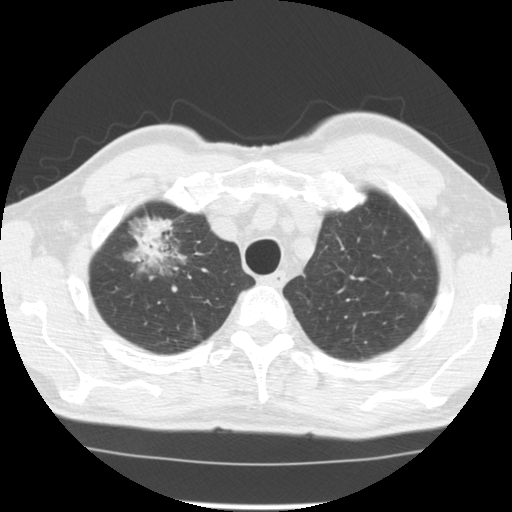
Axial slice from a low-dose chest CT screening exam; third annual screen; lung window (W 1500 / L -600 HU); 2.5 mm slice thickness; standard (soft-tissue) reconstruction kernel (STANDARD); 120 kVp; slice 24 of 128 in the series; 512 × 512 image matrix. Male participant, aged 64 years at enrolment. Former smoker at enrolment.
Lesion marked by an expert reader, box from (x=124, y=227) to (x=198, y=288) px. The screening reader recorded 3 non-calcified nodules or masses ≥4 mm on this exam; which of them this box marks is not recorded. Official screen result: positive, other. Later outcome: lung cancer diagnosed 30 days after this screen — adenocarcinoma, NOS, right upper lobe, well differentiated (G1), stage IB (AJCC 6th edition), 45 mm at pathology.